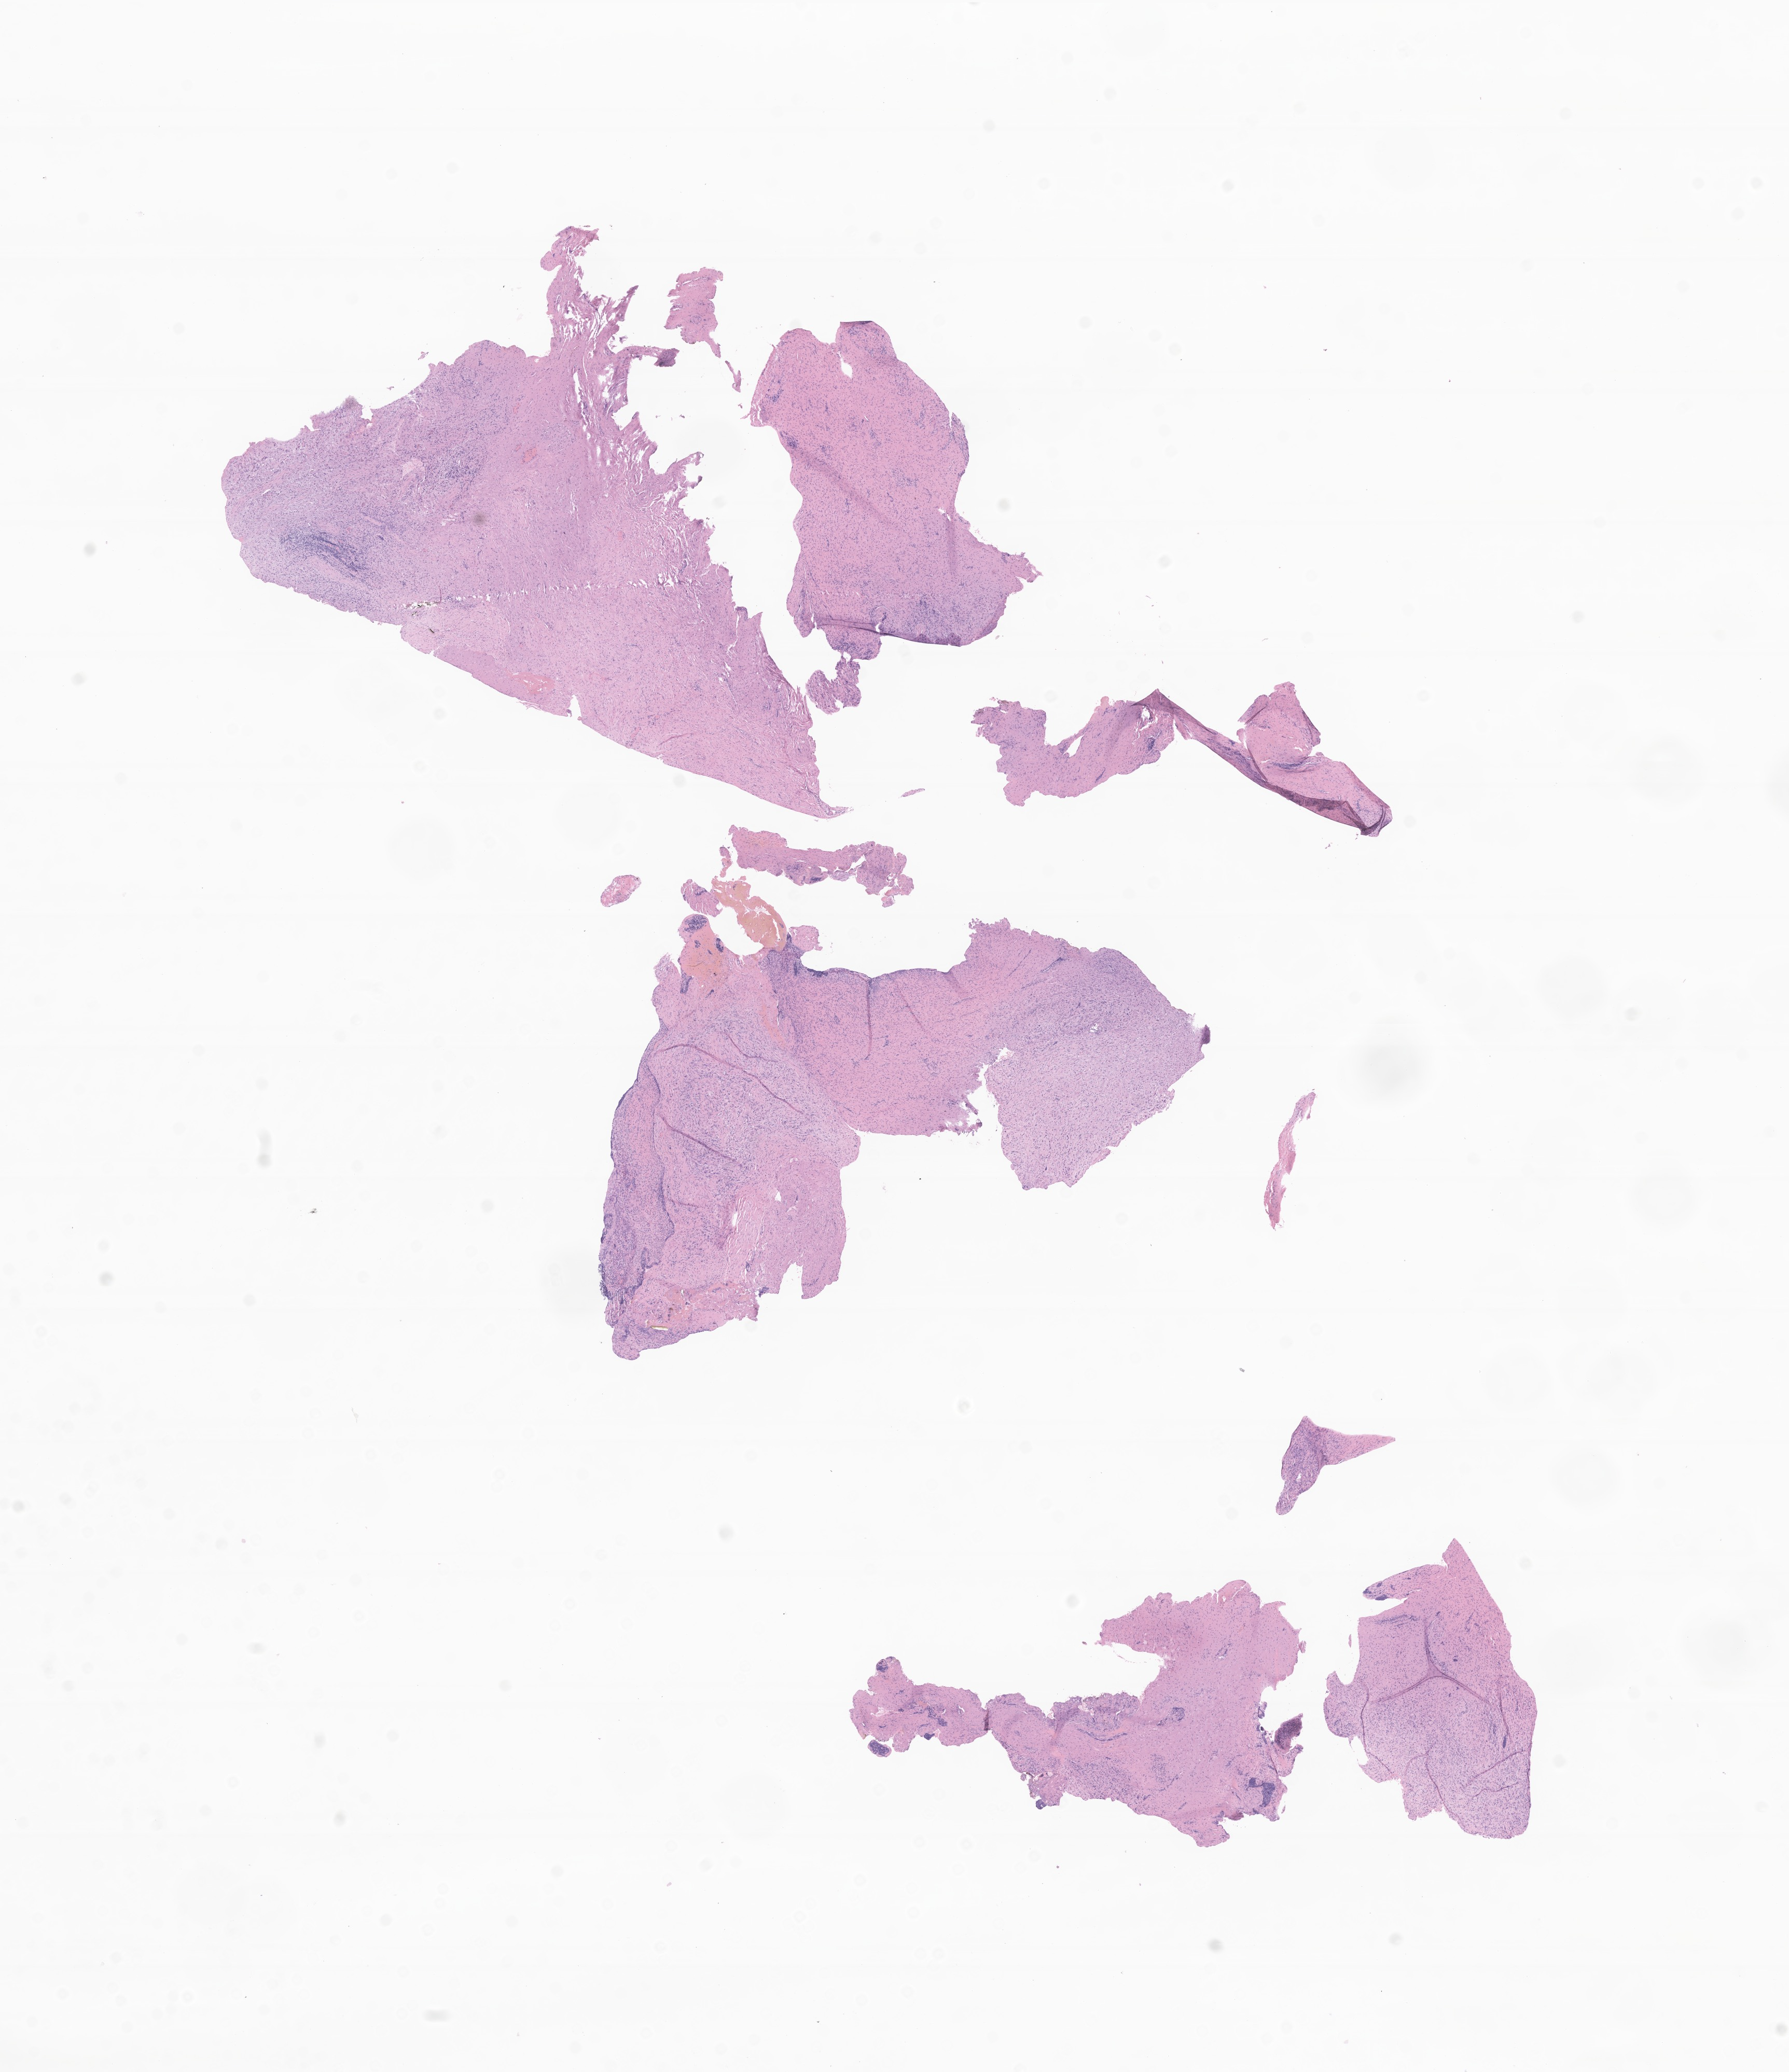
Whole-slide image, haematoxylin and eosin stain of tumor tissue from the urinary bladder — low-resolution overview of the scanned area, about 14.5 x 16.8 mm; FFPE section. Male patient, age 37 months.
Recorded diagnosis: Embryonal rhabdomyosarcoma, NOS.